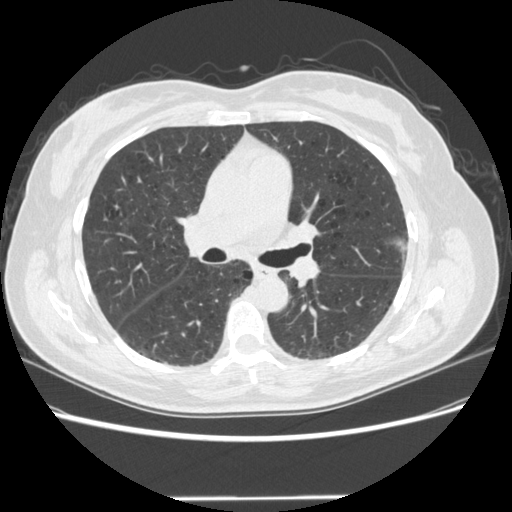
Chest CT (low-dose screening protocol), one axial image, first (baseline) screen, lung window (W 1500 / L -600 HU), 1.25 mm slice thickness, 120 kVp, slice 185 of 301 in the series. Female participant, aged 61 years at enrolment. Current smoker at enrolment.
• Expert-annotated lung lesion, box from (x=383, y=228) to (x=428, y=278) px.
• No non-calcified nodule or mass ≥4 mm was recorded by the screening reader at this exam.
• Official screen result: negative screen, minor abnormalities not suspicious for lung cancer.
• Later outcome: lung cancer diagnosed 791 days after this screen — bronchiolo-alveolar adenocarcinoma, NOS, left upper lobe, well differentiated (G1), stage IA (AJCC 6th edition), 11 mm at pathology.